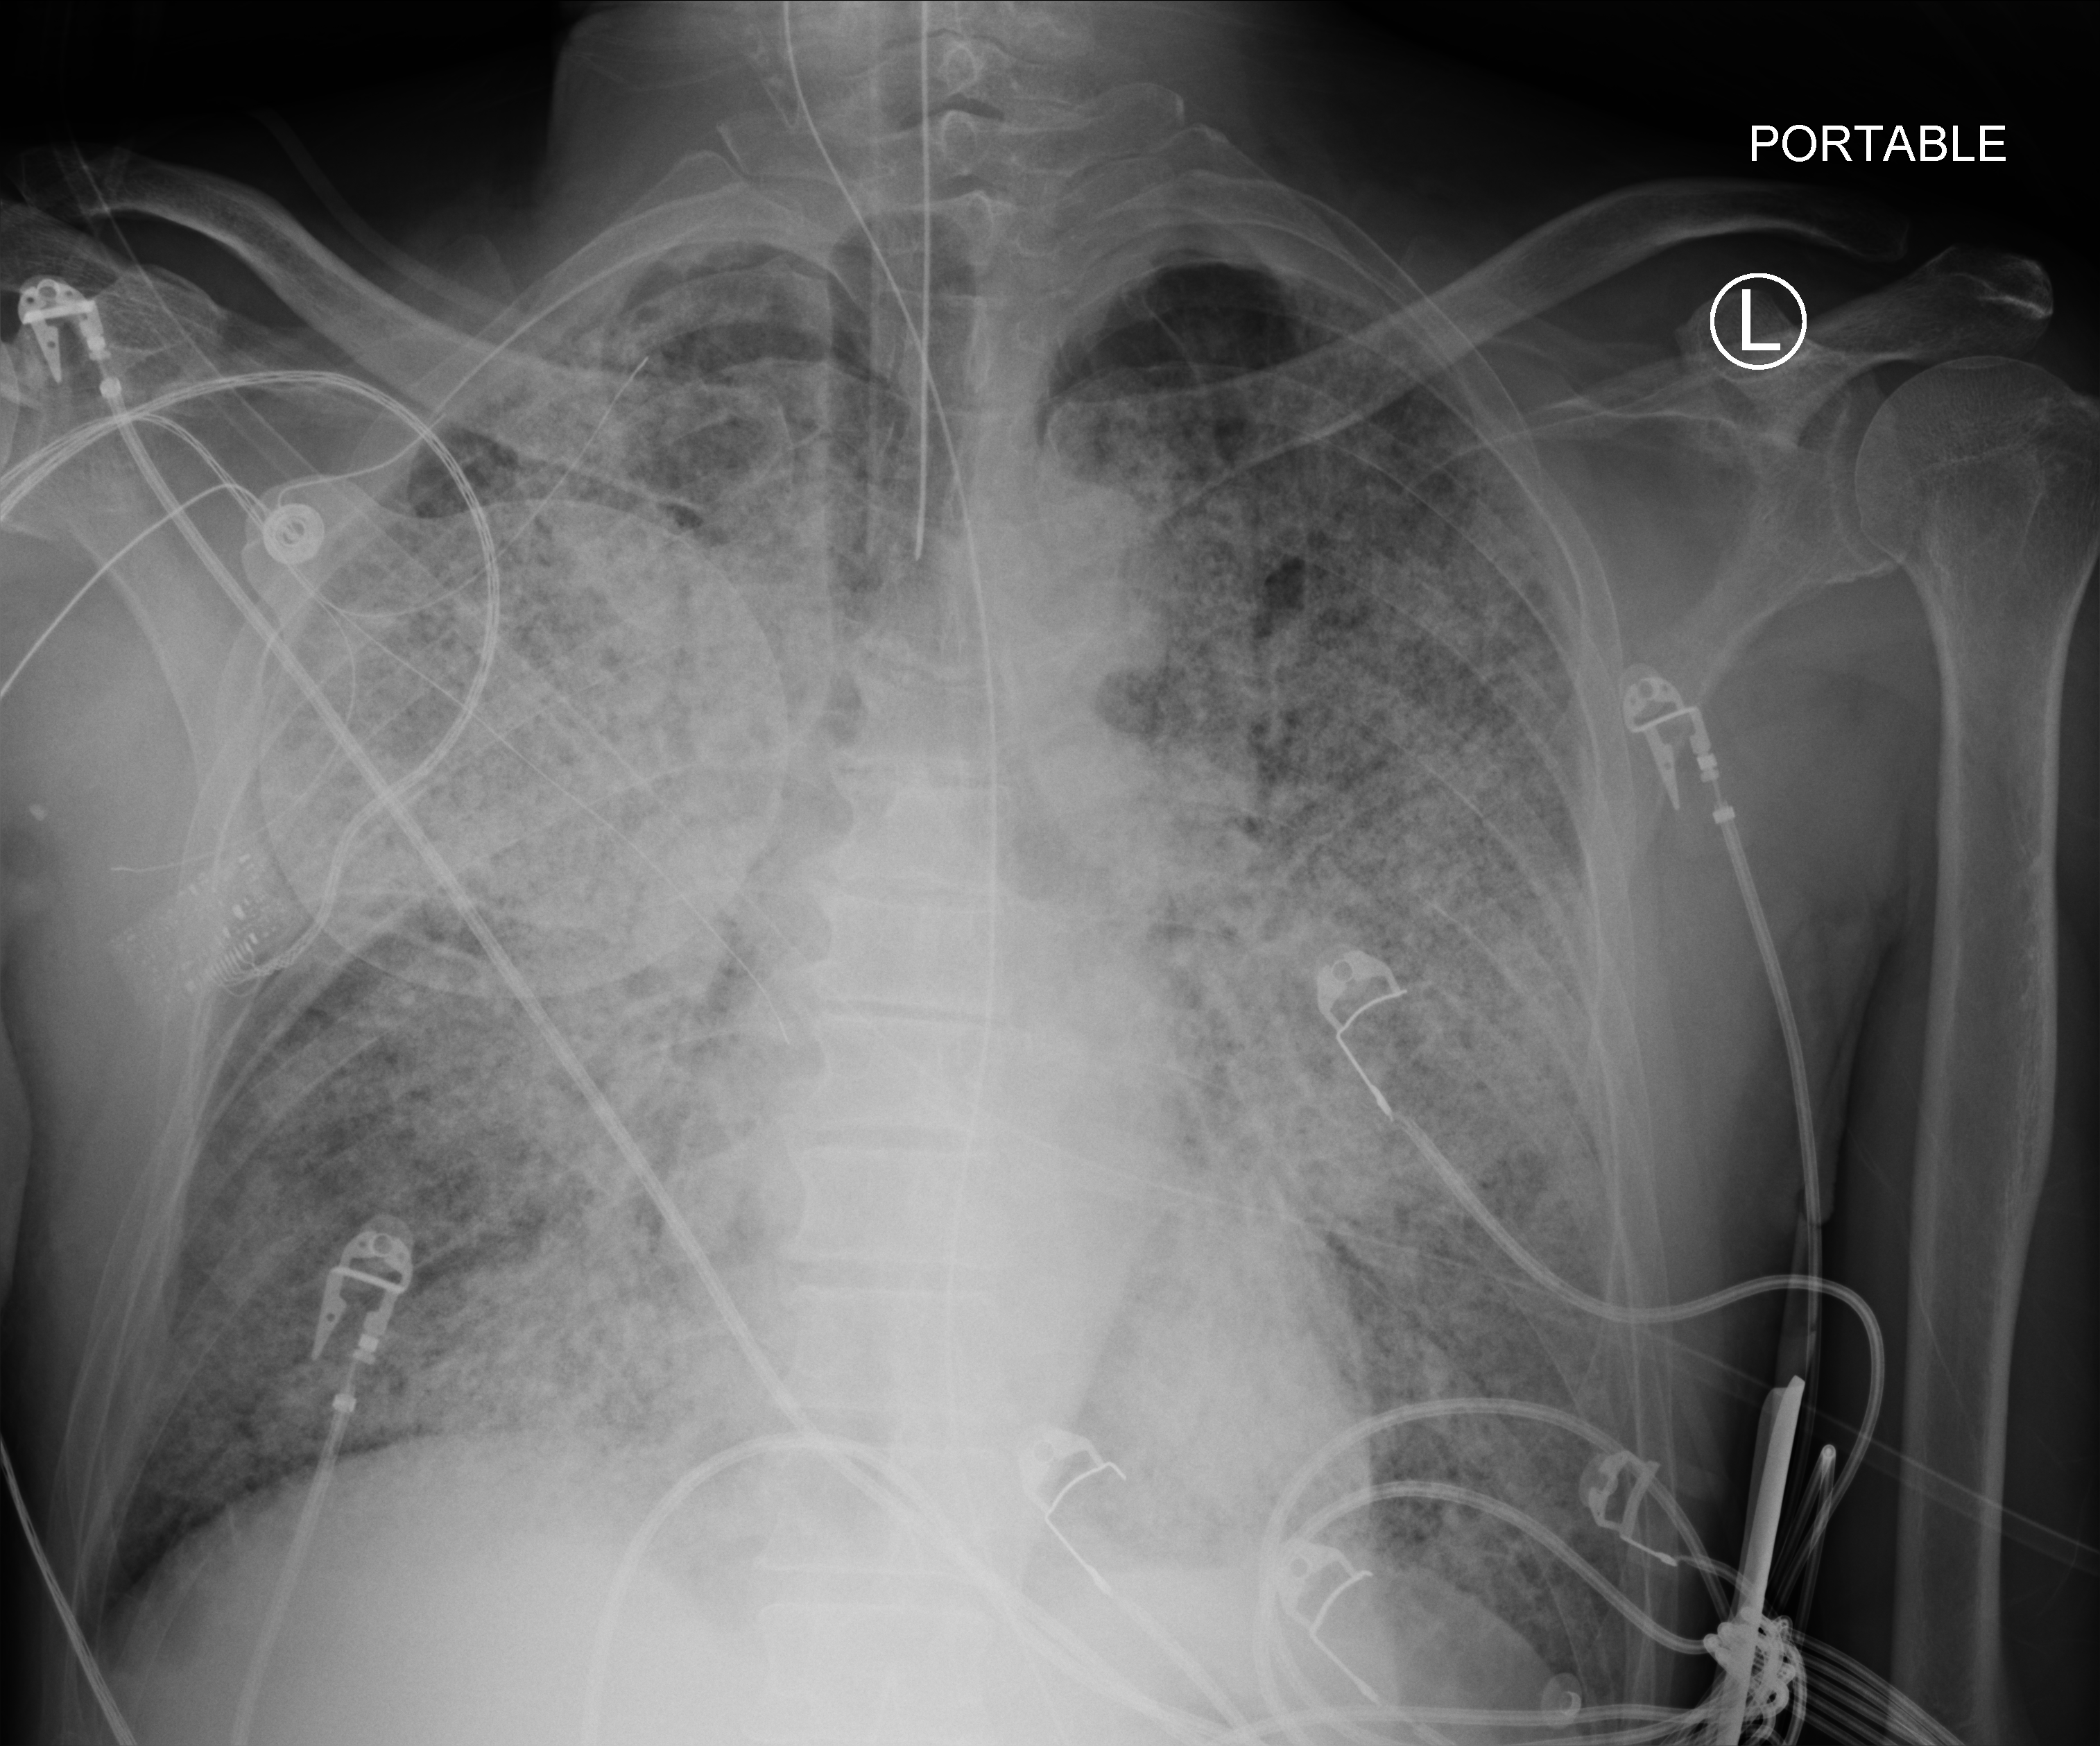
Bedside chest radiograph (computed radiography); anteroposterior (AP) projection. Patient hospitalised with COVID-19; male, aged 60–74 years.
Admission-level facts for this patient (not findings on this image; timing relative to this image not recorded):
- hypertension (admission record): no